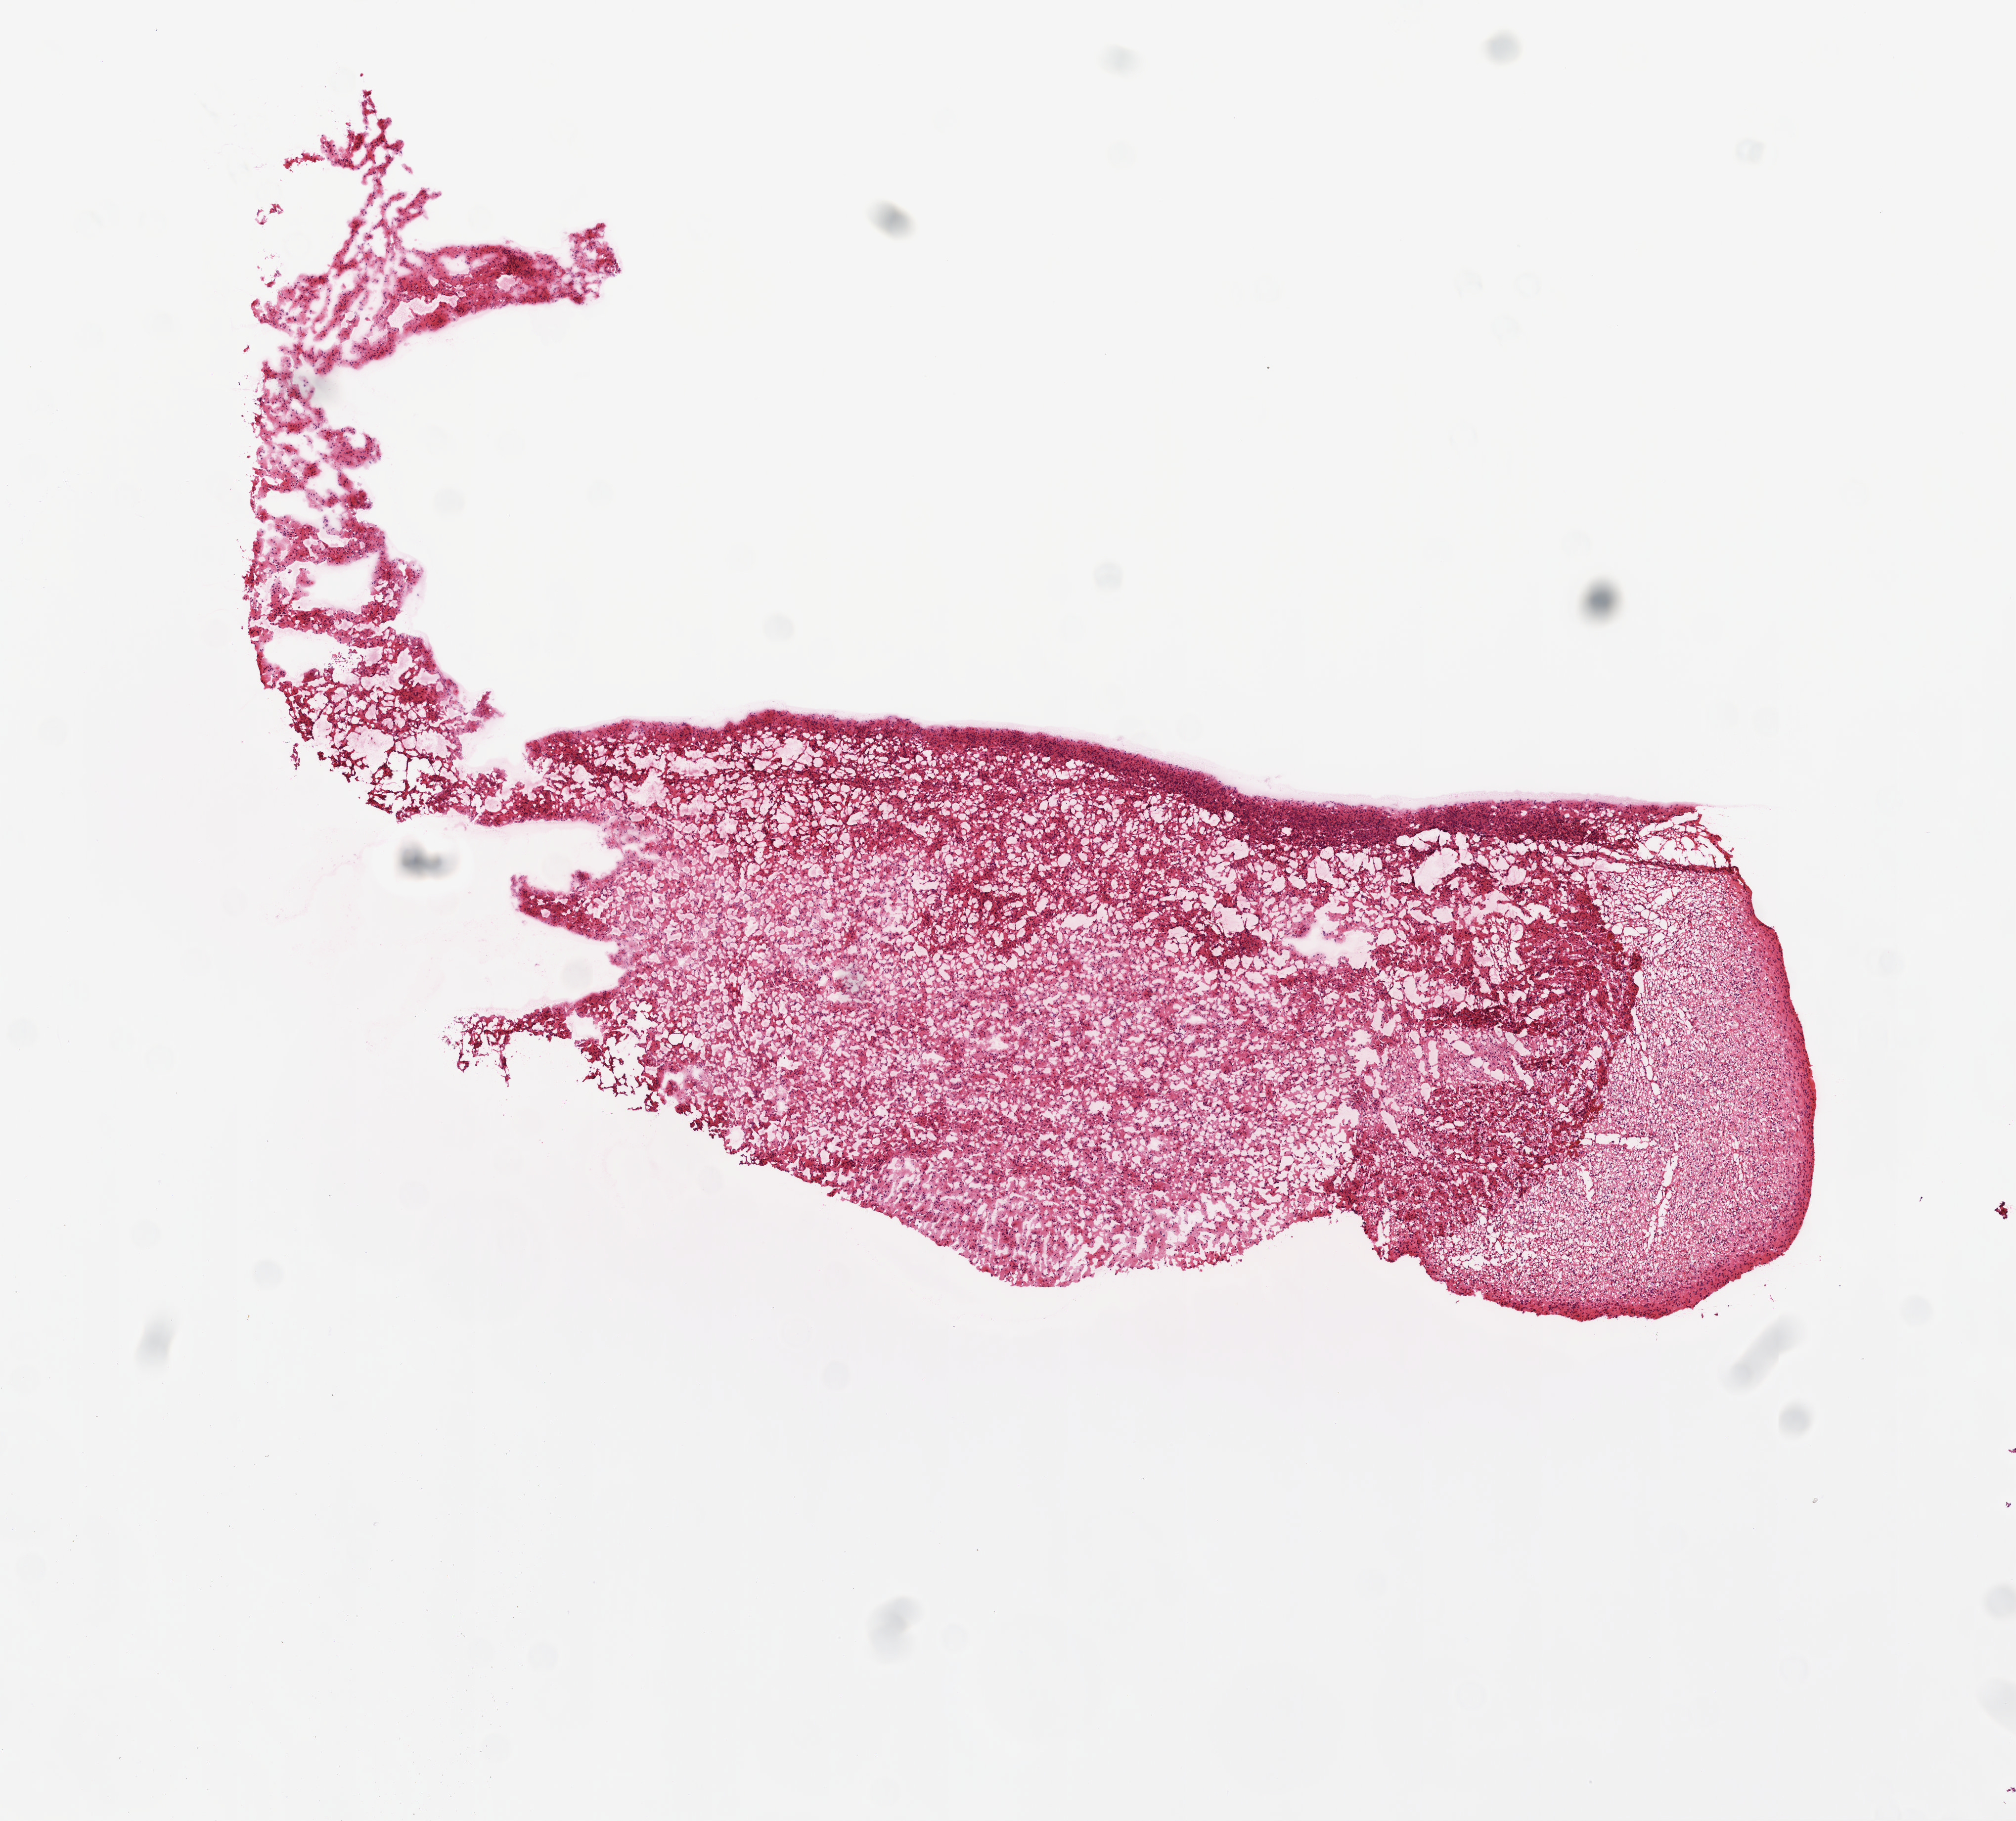
Whole-slide histology image, H&E-stained — shown as a low-resolution overview of the whole scanned area (about 8.2 x 7.4 mm), frozen section from the top of the tissue portion, brain, primary tumour sample. Patient: male, age at initial diagnosis 64 years. Pathologist review of this section (percent, as recorded): tumour cells 80%, tumour nuclei 85%.
Diagnosis: Glioblastoma.